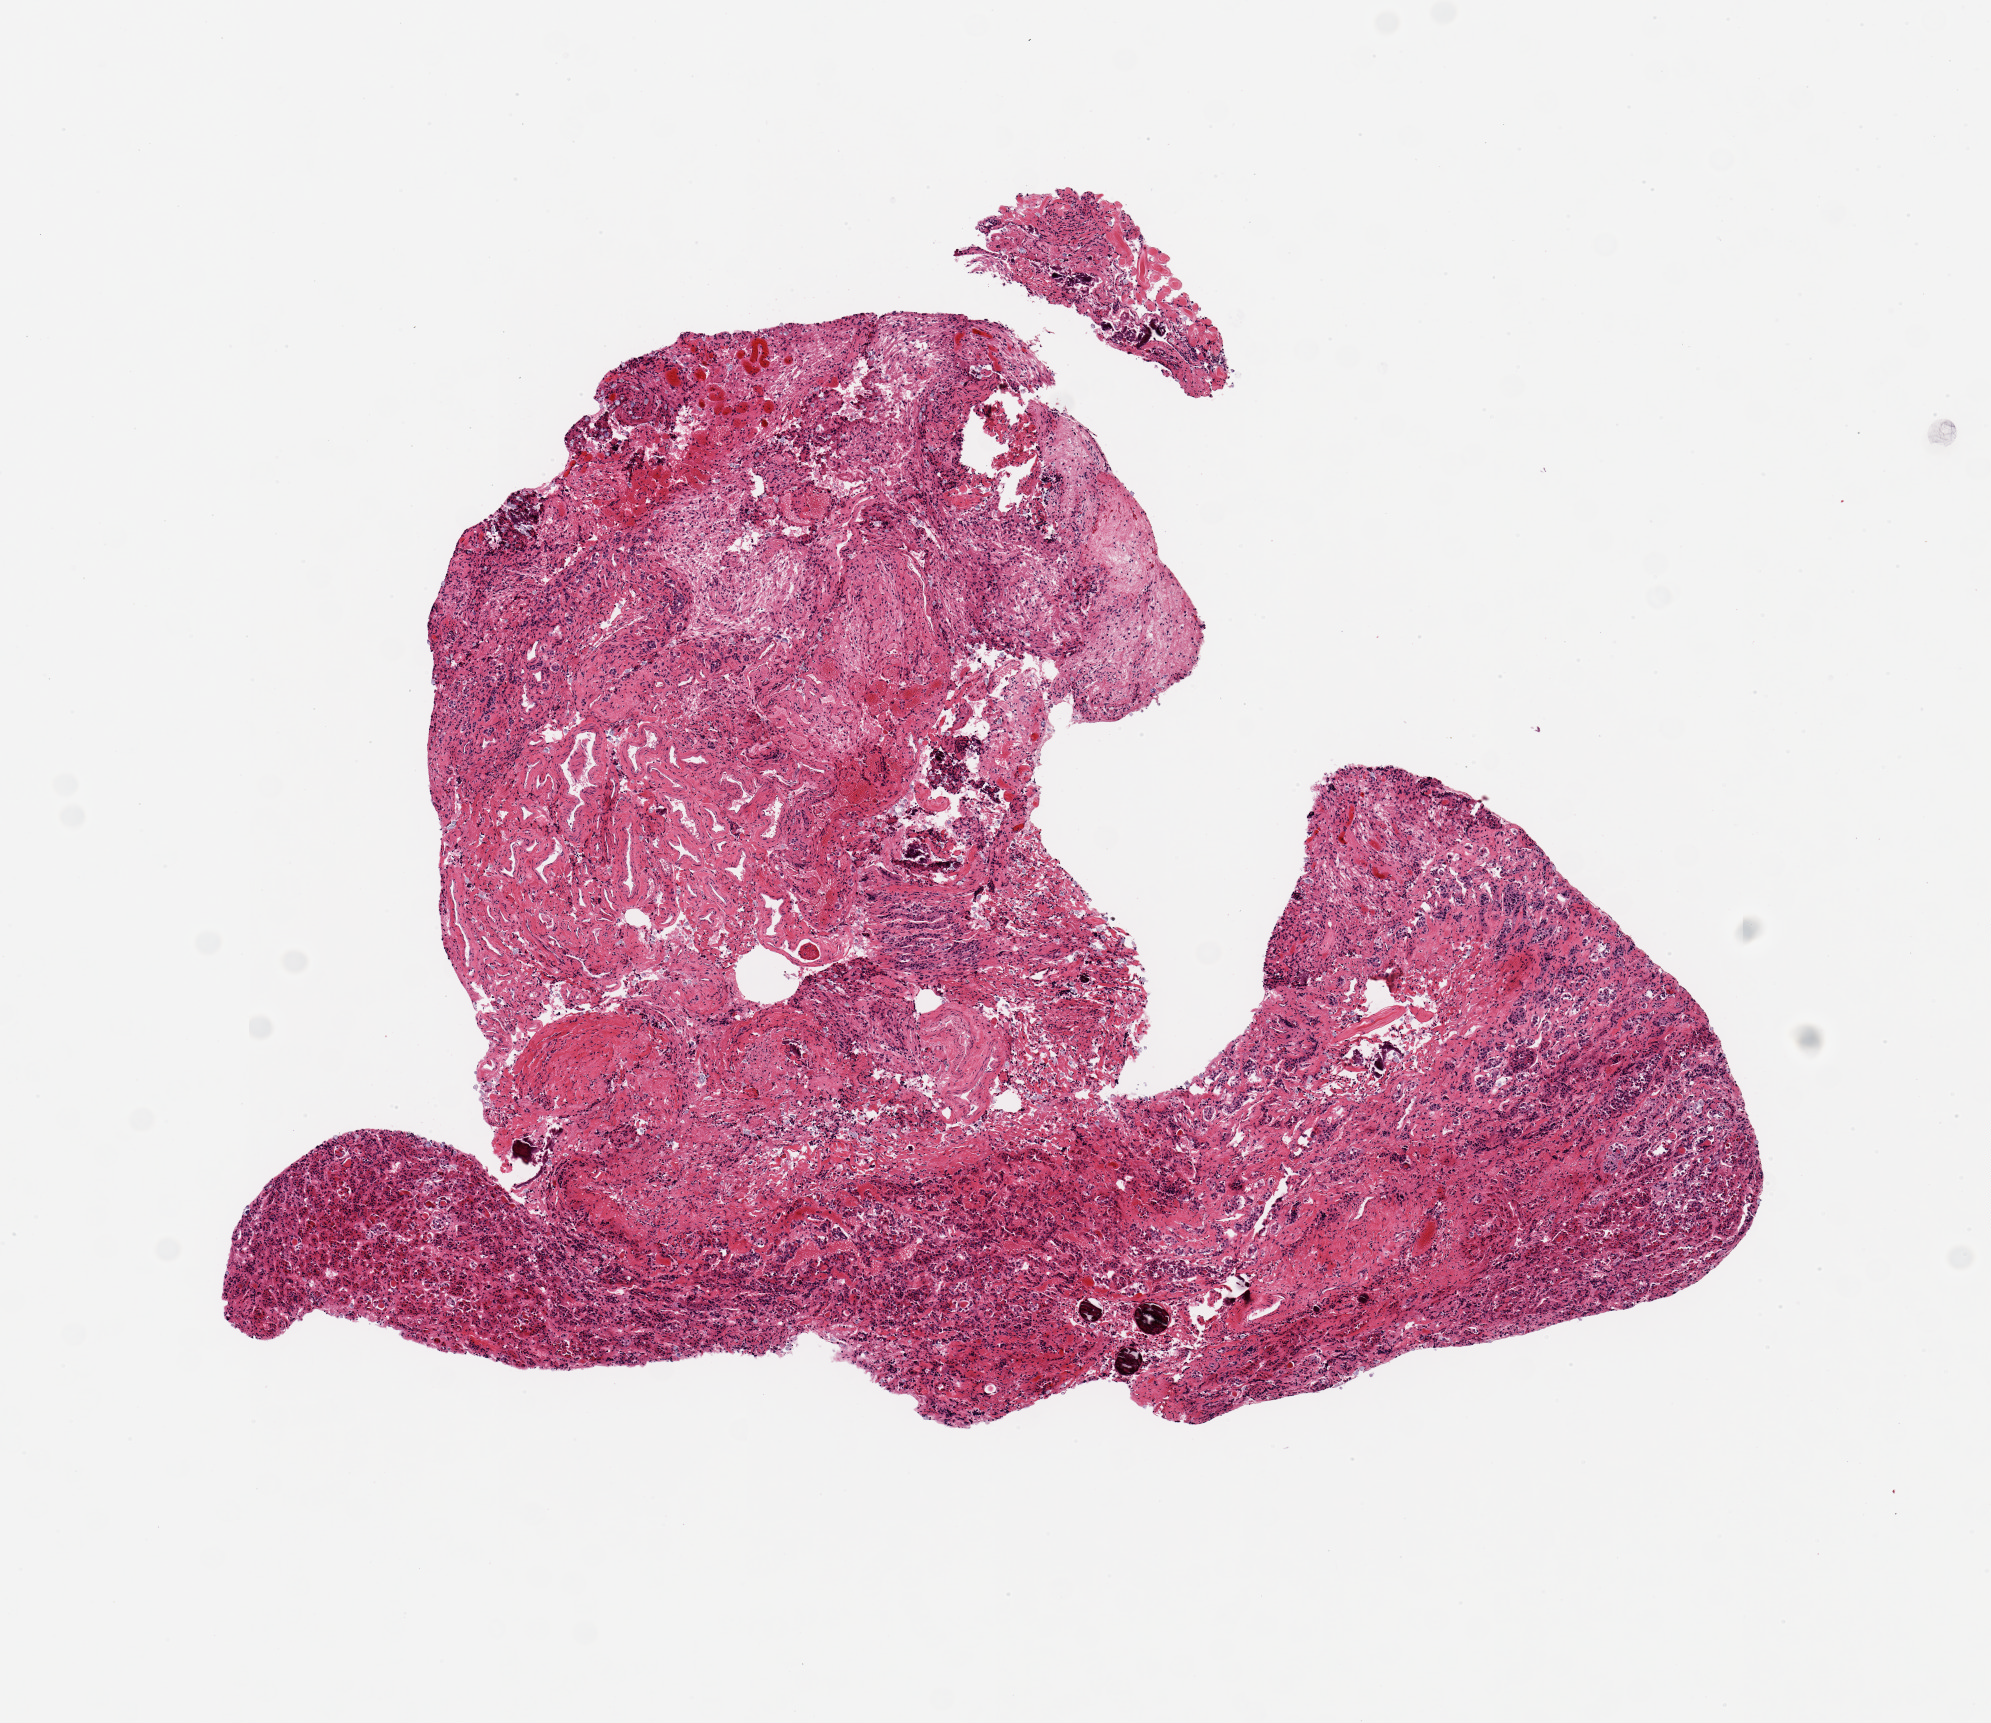
Digitized hematoxylin and eosin (H&E)-stained section — a low-resolution overview of the entire scanned area, about 7.9 x 6.8 mm (acquisition: 20x scan); PAXgene-fixed paraffin-embedded (PFPE) section; section of pituitary (target tissue); tissue donor sample. Donor sex: female.
Reviewer comment on this tissue sample: 2 piece ~5x5 mm. Mixed adeno/neurohypophysis, mixed in dural elements (vessels).